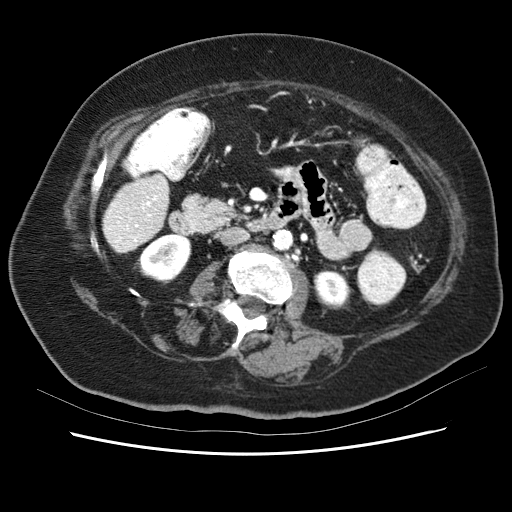
Contrast-enhanced abdominal CT (liver protocol), one axial slice; position 12 of 62 along the scan axis; reconstruction kernel STANDARD; 120 kVp; soft-tissue window (W 400 / L 40 HU); 2.5 mm slice thickness; 512 × 512 image matrix. From the clinical record (not read from this slice): diagnosis: hepatocellular carcinoma (patient treated with transarterial chemoembolisation; whether this scan precedes or follows treatment is not stated here); TNM stage (as recorded): Stage-I; Child-Pugh class: B; tumour nodularity: uninodular; tumour size: 5.3 cm.
Outlined on this slice (semi-automatically segmented with operator editing):
- liver parenchyma outside the tumour (the mass and vessels are separate outlines, so this box may not span the whole liver): bounding box (x1, y1, x2, y2) in pixels: (100, 170, 168, 256)
- liver vessels: (104, 175, 166, 251)